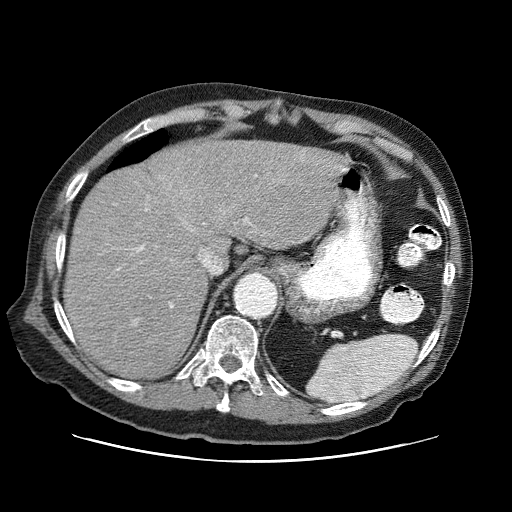
Contrast-enhanced abdominal CT (liver protocol), one axial slice. Reconstruction kernel STANDARD. One of 3 acquisitions stored at this slice position. Soft-tissue window (W 400 / L 40 HU). 2.5 mm slice thickness. 512 × 512 image matrix. From the clinical record (not read from this slice): diagnosis: hepatocellular carcinoma (patient treated with transarterial chemoembolisation; whether this scan precedes or follows treatment is not stated here); TNM stage (as recorded): Stage-IIIA; Child-Pugh class: A; tumour differentiation: well differentiated; tumour nodularity: multinodular.
Annotated regions visible in this slice (semi-automatic segmentation, software-assisted and operator-edited):
- abdominal aorta: box from (x=237, y=276) to (x=275, y=318) px
- liver parenchyma outside the tumour (the mass and vessels are separate outlines, so this box may not span the whole liver): (x=64, y=140)–(x=346, y=378)
- liver vessels: (x=118, y=169)–(x=345, y=308)